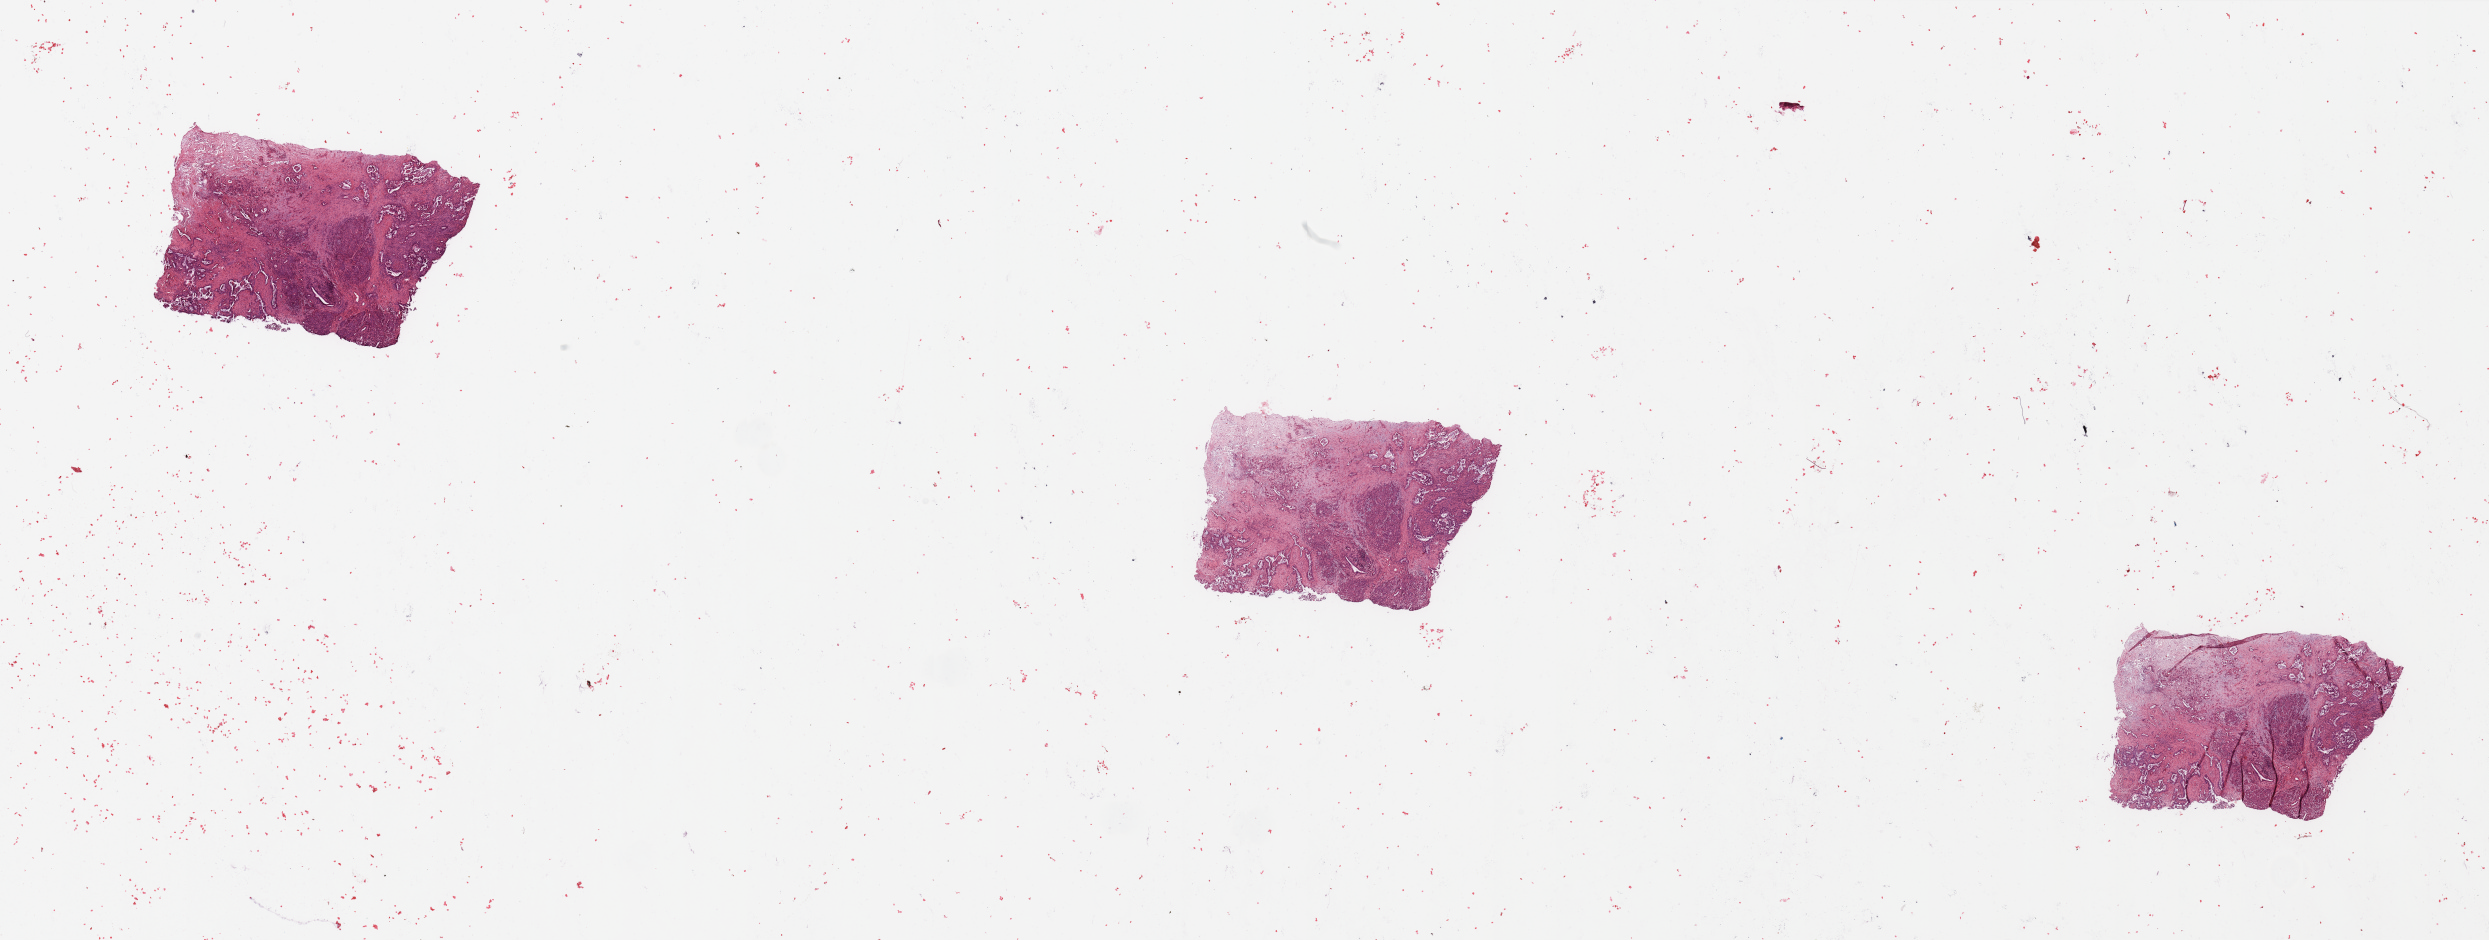
H&E-stained whole-slide image, whole scanned area (about 39.4 x 14.9 mm, acquisition: 20x scan) shown as a low-resolution overview. Tumour tissue sample, sampled site: pancreas. 61-year-old male patient. Histologic grade: G3 (poorly differentiated). Slide review estimates, as recorded: tumour nuclei 25%, necrosis 2%.
* primary tumour site (as recorded): head
* histologic diagnosis: Infiltrating duct carcinoma, NOS
* AJCC pathologic stage: III